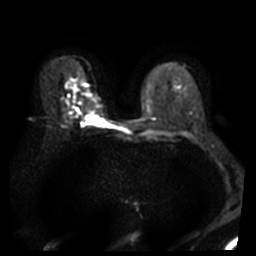
Breast MRI, one axial slice; slice 24 of 46 in the series (ordered by position); diffusion-weighted series; image 2 of 4 stored at this slice position (different b-values; order by instance number); 3 T; 5 mm slice thickness; 256 × 256 image matrix. Female patient.
Outlined on this slice (expert manual segmentation):
- tumour on diffusion-weighted imaging: bounding box <87,116,103,122> (left, top, right, bottom; pixels)